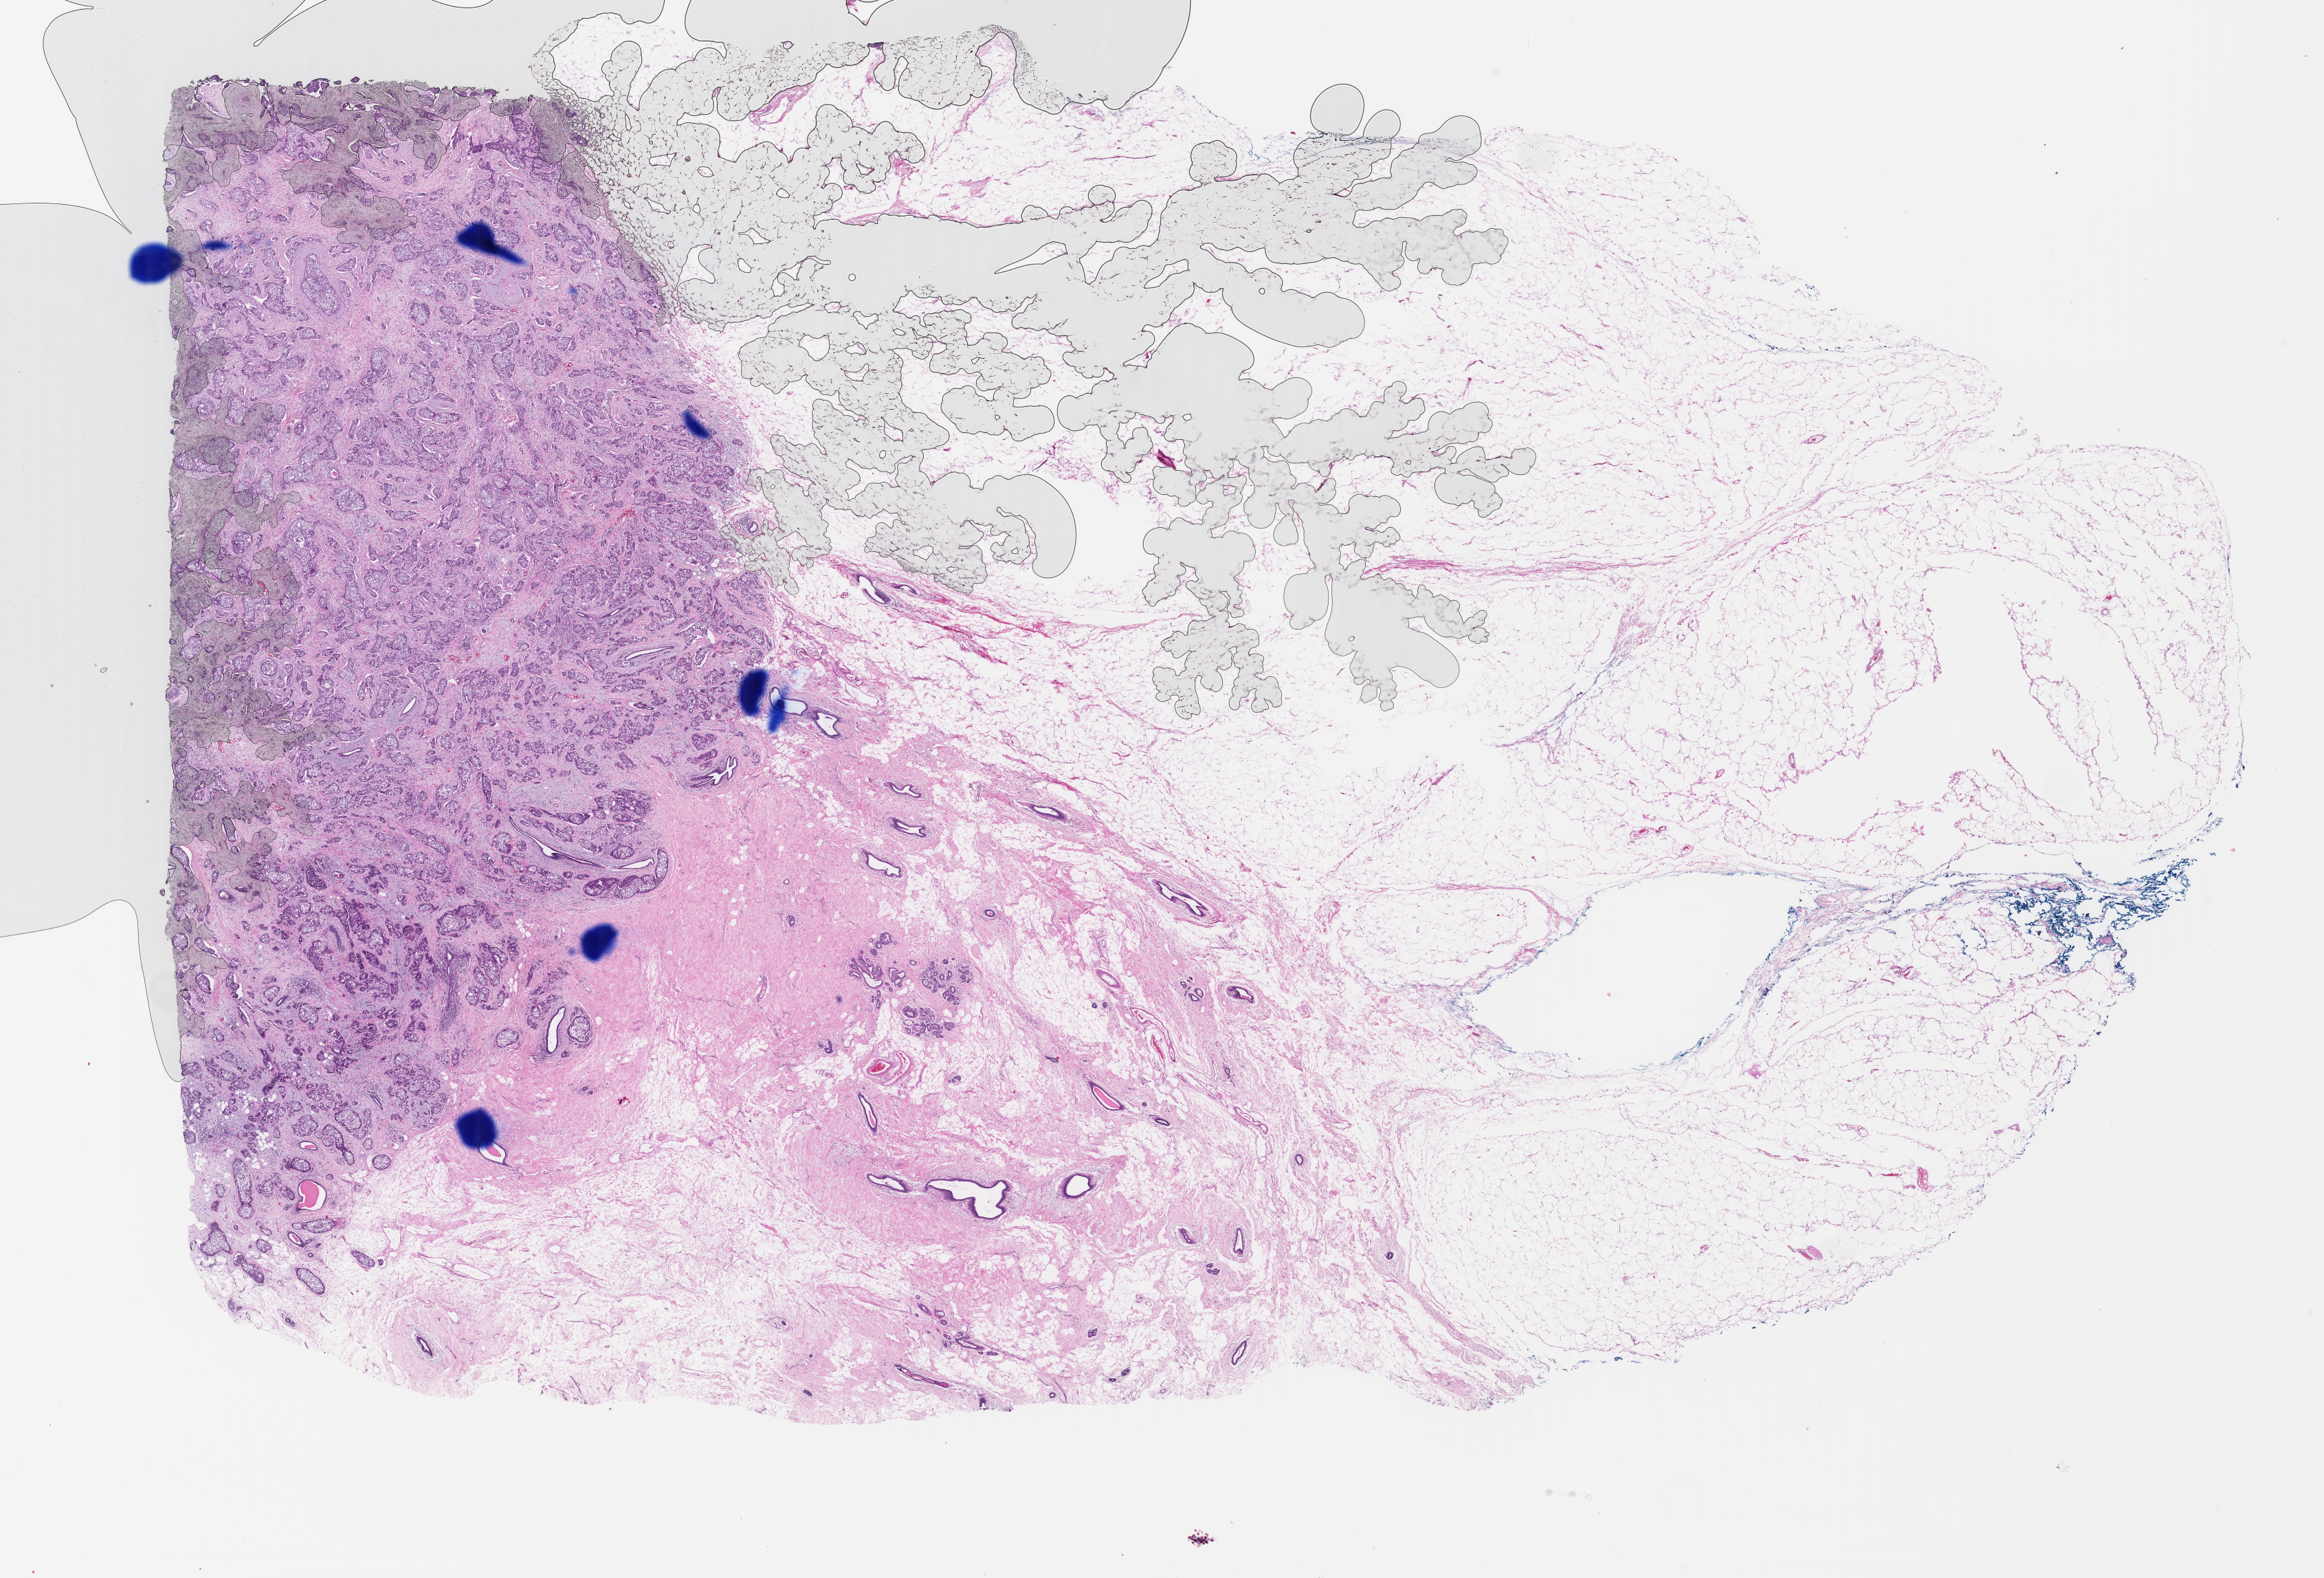
Digitized Hematoxylin and eosin (H&E) stained tissue section (whole slide), low-resolution overview of the scanned area, about 26.9 x 18.3 mm (from a 40x scan). FFPE section. Primary tumour sample from the breast. Female patient; age at initial diagnosis 66 years.
AJCC pathologic stage: IIA. Lymph nodes positive (case pathology): 0 of 17 examined. Pathologic diagnosis: Infiltrating duct carcinoma, NOS.